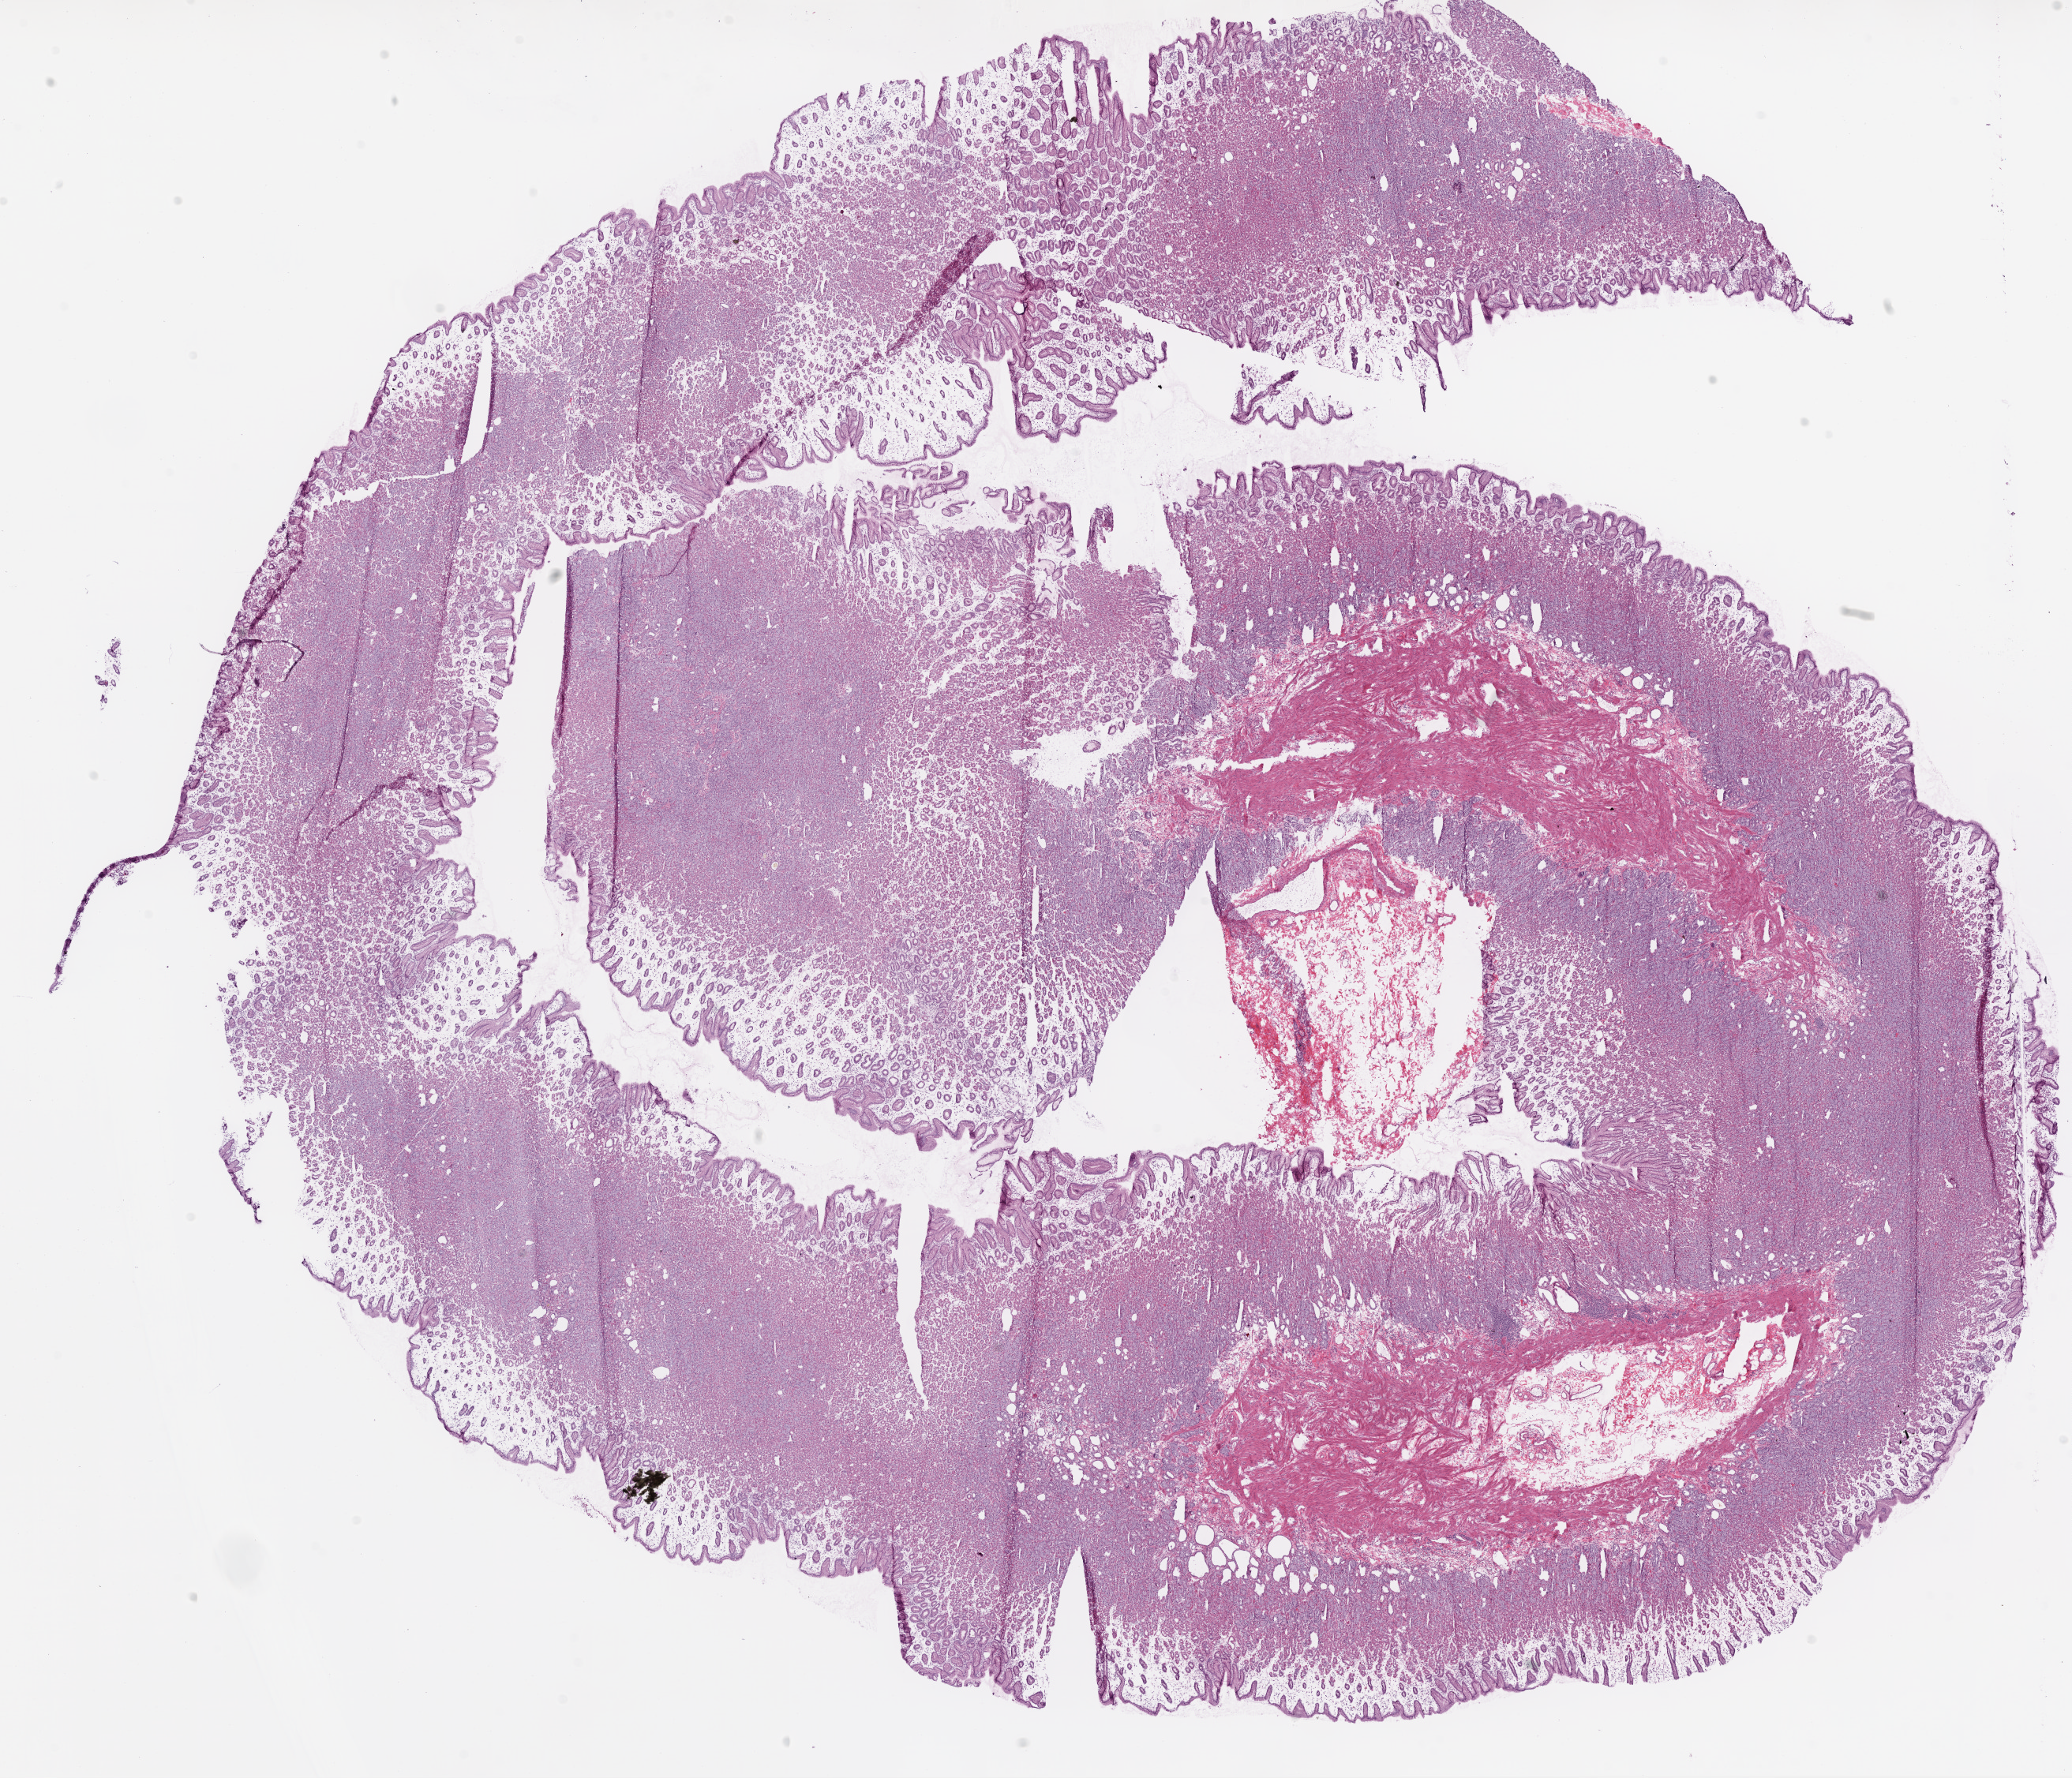
Digitized H&E-stained tissue section (whole slide) — a low-resolution overview of the entire scanned area, about 21.1 x 18.1 mm (from a 20x scan); frozen section from the top of the tissue portion; sample: solid tissue normal (non-tumour tissue), stomach. Female, age 55 years at initial diagnosis.
This section: solid tissue normal (non-tumour) sample from the same patient. Patient diagnosis: Adenocarcinoma, NOS (cardia, NOS).